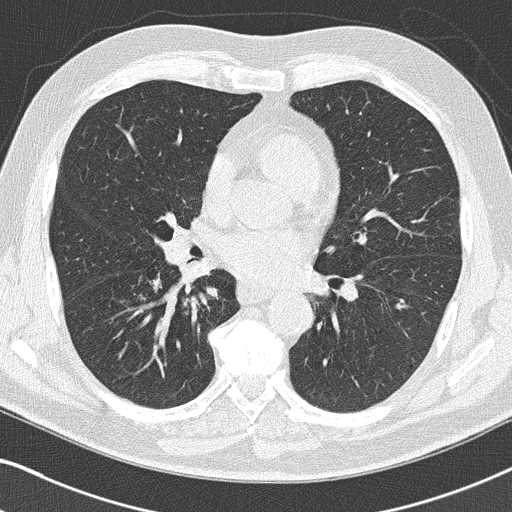
Low-dose screening chest CT, axial slice; third annual screen; lung window (W 1500 / L -600 HU); 2 mm slice thickness; lung (sharp) reconstruction kernel (B50f); 120 kVp; slice 88 of 155 in the series. Male, age 66 years at enrolment.
- Expert reader's lesion annotation, bounding box (x1, y1, x2, y2) in pixels: (138, 266, 229, 329).
- Screening reader's record for this exam (one nodule recorded; not confirmed to be the boxed lesion): non-calcified nodule or mass ≥4 mm, right upper lobe, 5 × 4 mm, smooth margins, pre-existing on the prior screen: yes; interval growth: no.
- Official screen result: positive, other.
- Later outcome: lung cancer diagnosed 38 days after this screen — squamous cell carcinoma, NOS, right lower lobe, poorly differentiated (G3), stage IIA (AJCC 6th edition), 22 mm at pathology.